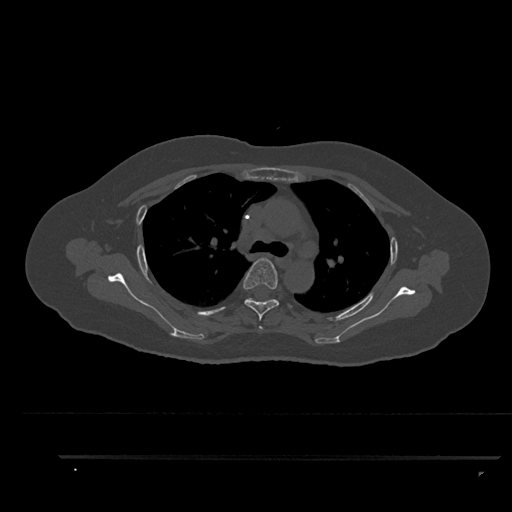
CT including the spine, one axial slice; slice 638 of 797 in the series (ordered by position); reconstruction kernel Br40s/3; 120 kVp; bone window (W 1800 / L 400 HU); 0.5 mm slice thickness; 512 × 512 image matrix, field of view 408 × 408 mm. Female patient, age 44 years. From the clinical record (not read from this slice): primary cancer: renal; vertebrae with lytic lesions (as recorded): L1.
Outlined on this slice (semi-automatic segmentation, software-assisted and operator-edited):
- T3 vertebra: box from (x=259, y=326) to (x=263, y=330) px
- T4 vertebra: (x=242, y=258)–(x=279, y=321)
- T5 vertebra: (x=245, y=298)–(x=249, y=301)